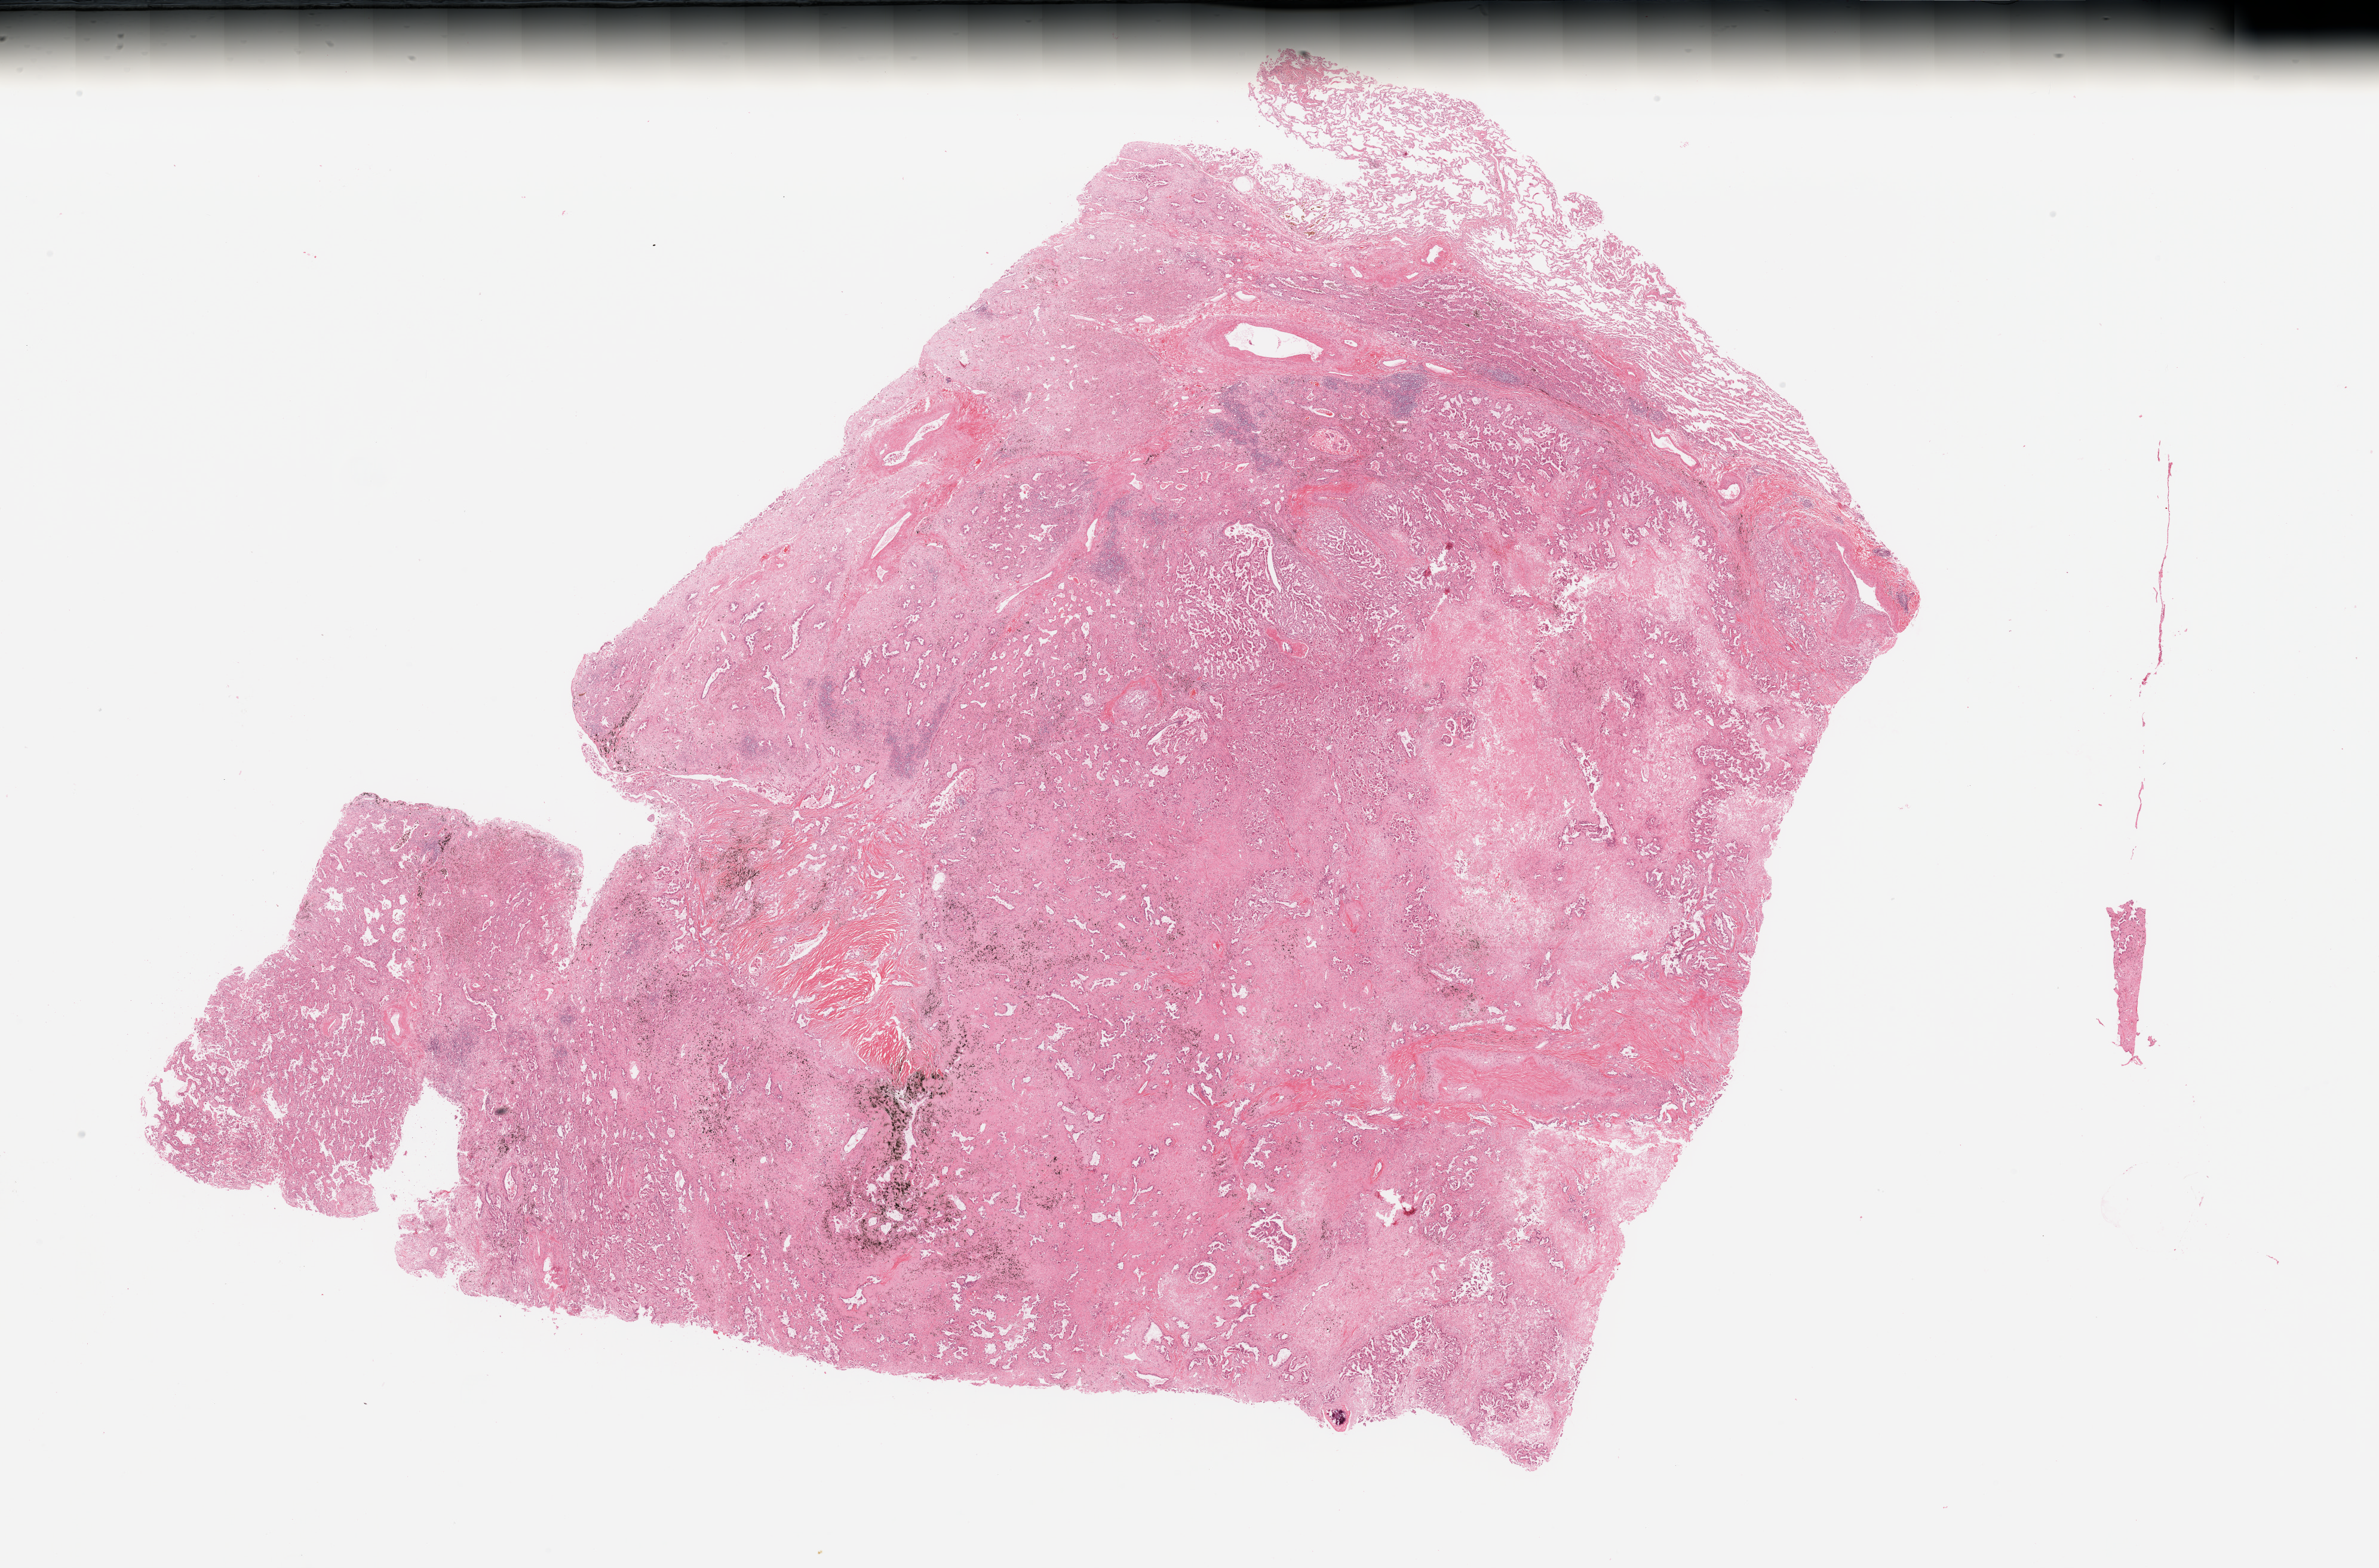
H&E whole-slide image — a low-resolution overview of the entire scanned area, about 31.5 x 20.8 mm (slide scanned at 20x). Tumour tissue sample, sampled site: lung. 69-year-old female patient. Histologic grade: G2 (moderately differentiated). Composition of this section per pathologist review: tumour nuclei 65%, necrosis 15%.
• AJCC pathologic stage: IIIA
• histologic diagnosis: Adenocarcinoma, NOS